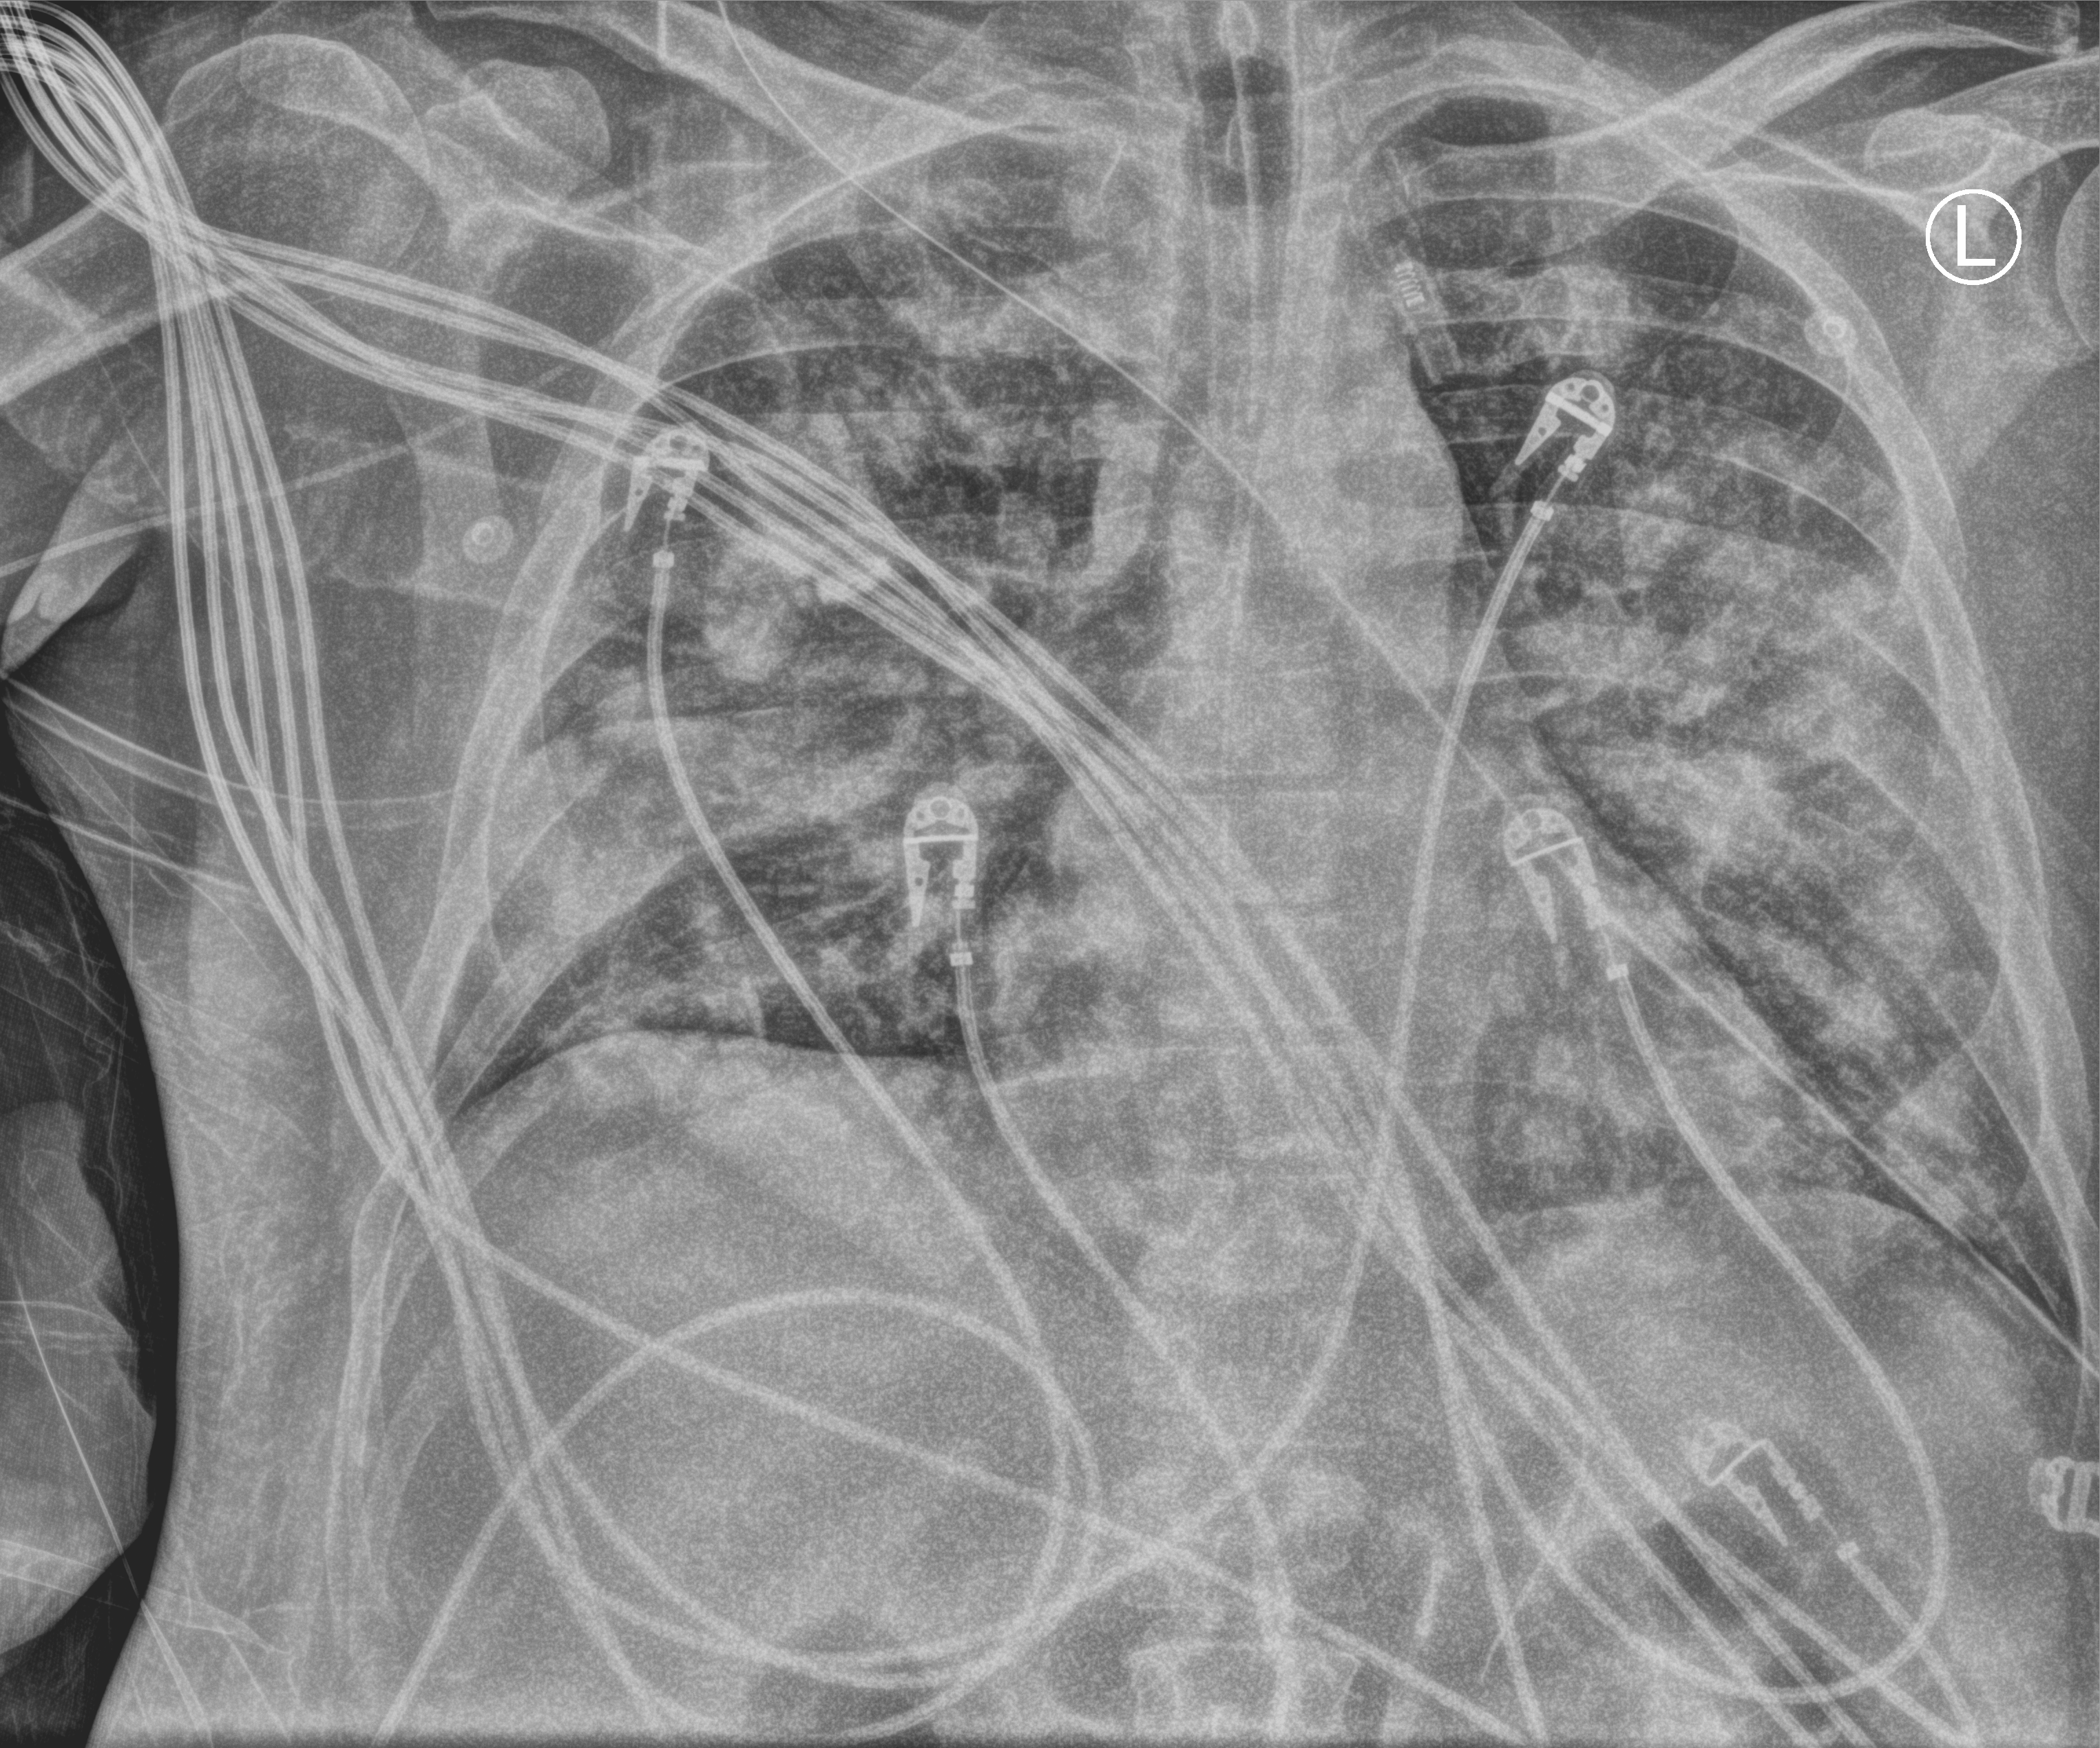
Bedside chest radiograph (computed radiography), anteroposterior (AP) projection. Male patient hospitalised with COVID-19, age 18–59 years.
From the hospital-stay record, not from the radiograph (when in the stay this image was taken is not recorded): other chronic lung disease (admission record): no; admitted to intensive care during this hospital stay: yes.